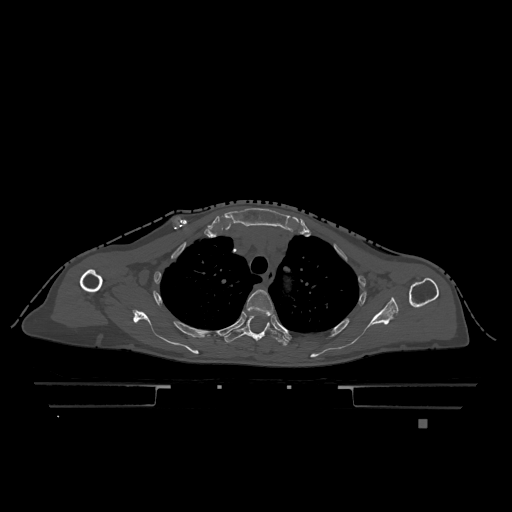
CT including the spine, one axial slice. Slice 899 of 1317 in the series (ordered by position). Bone window (W 1800 / L 400 HU). 0.5 mm slice thickness. 512 × 512 image matrix, field of view 500 × 500 mm. Female patient, age 74 years. Case-level facts recorded for this patient, not image findings: primary cancer: lung; vertebrae with lytic lesions (as recorded): T1, T4, T5, T6, L4, L5.
Structures marked on this image (semi-automatically segmented with operator editing):
- T3 vertebra: bounding box (x1, y1, x2, y2) in pixels: (246, 289, 274, 316)
- T4 vertebra: (224, 315, 291, 346)